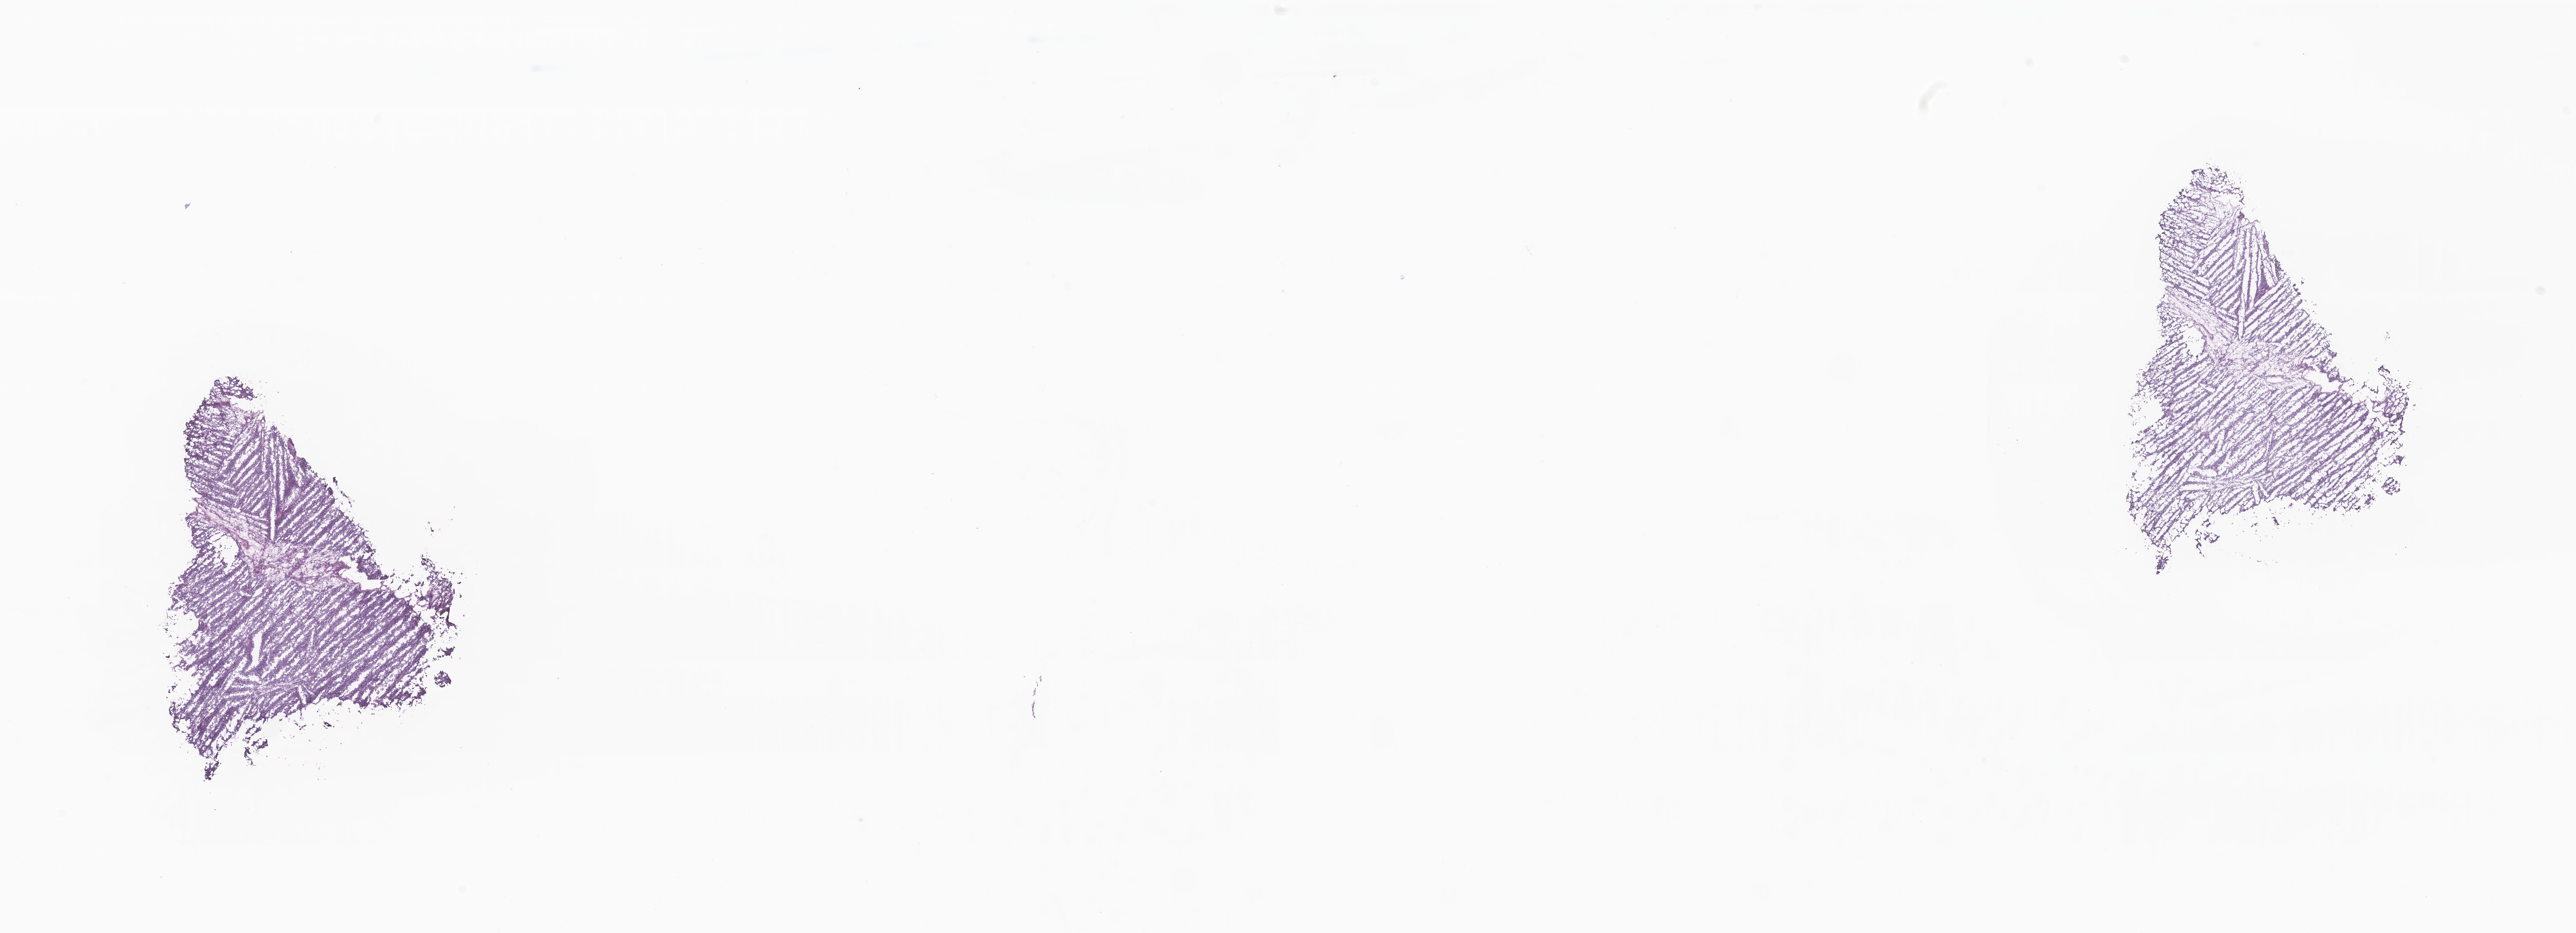
Whole-slide image, H&E stain of tumor tissue from the orbit — low-resolution overview of the scanned area, about 29.8 x 10.8 mm, cryosection (OCT / tissue freezing medium). Patient female; age 109 months.
• diagnosis (ICD-O-3 morphology term): Rhabdomyosarcoma, NOS